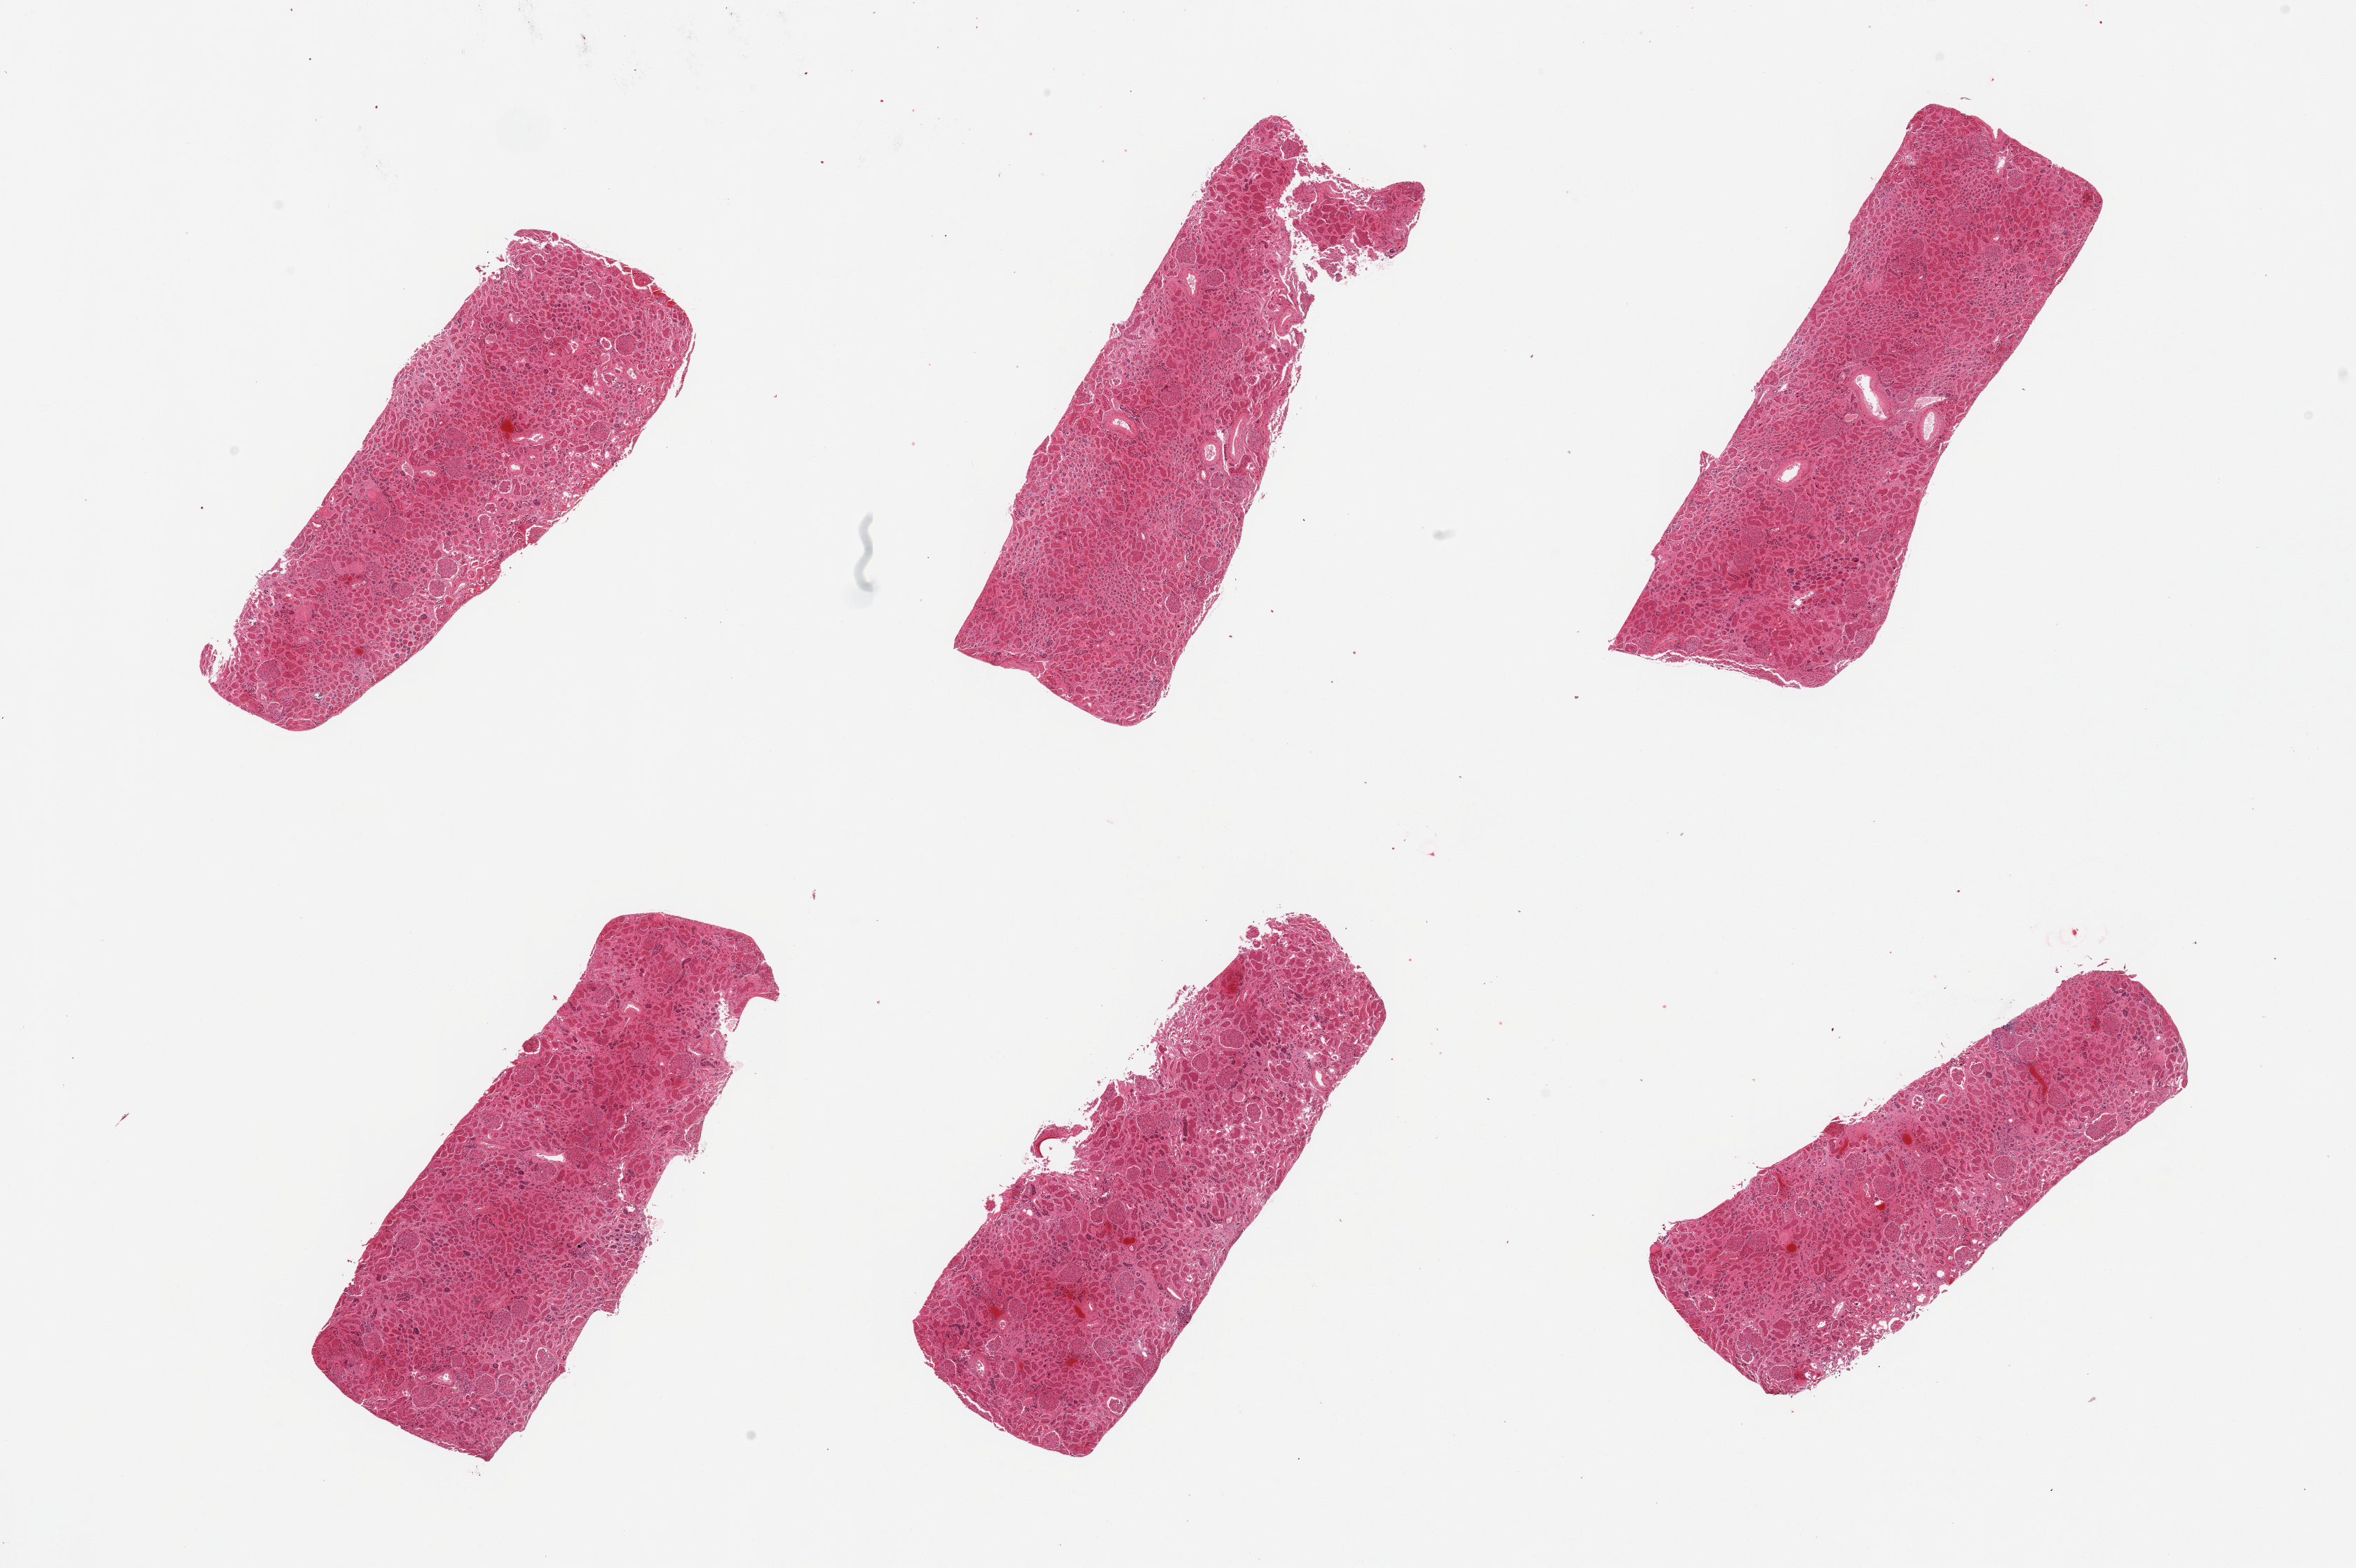
H&E whole-slide image, brightfield, shown as a low-resolution overview of the whole scanned area (about 26.6 x 17.7 mm, acquisition: 20x scan); PAXgene-fixed paraffin-embedded (PFPE) section; section of renal cortex (target tissue); tissue donor sample.
- review note (as recorded): 6 pieces; glomeruli in all sections, some sclerotic; tubules very autolyzed, cannot distinguish from acute tubular necrosis; arteriosclerosis